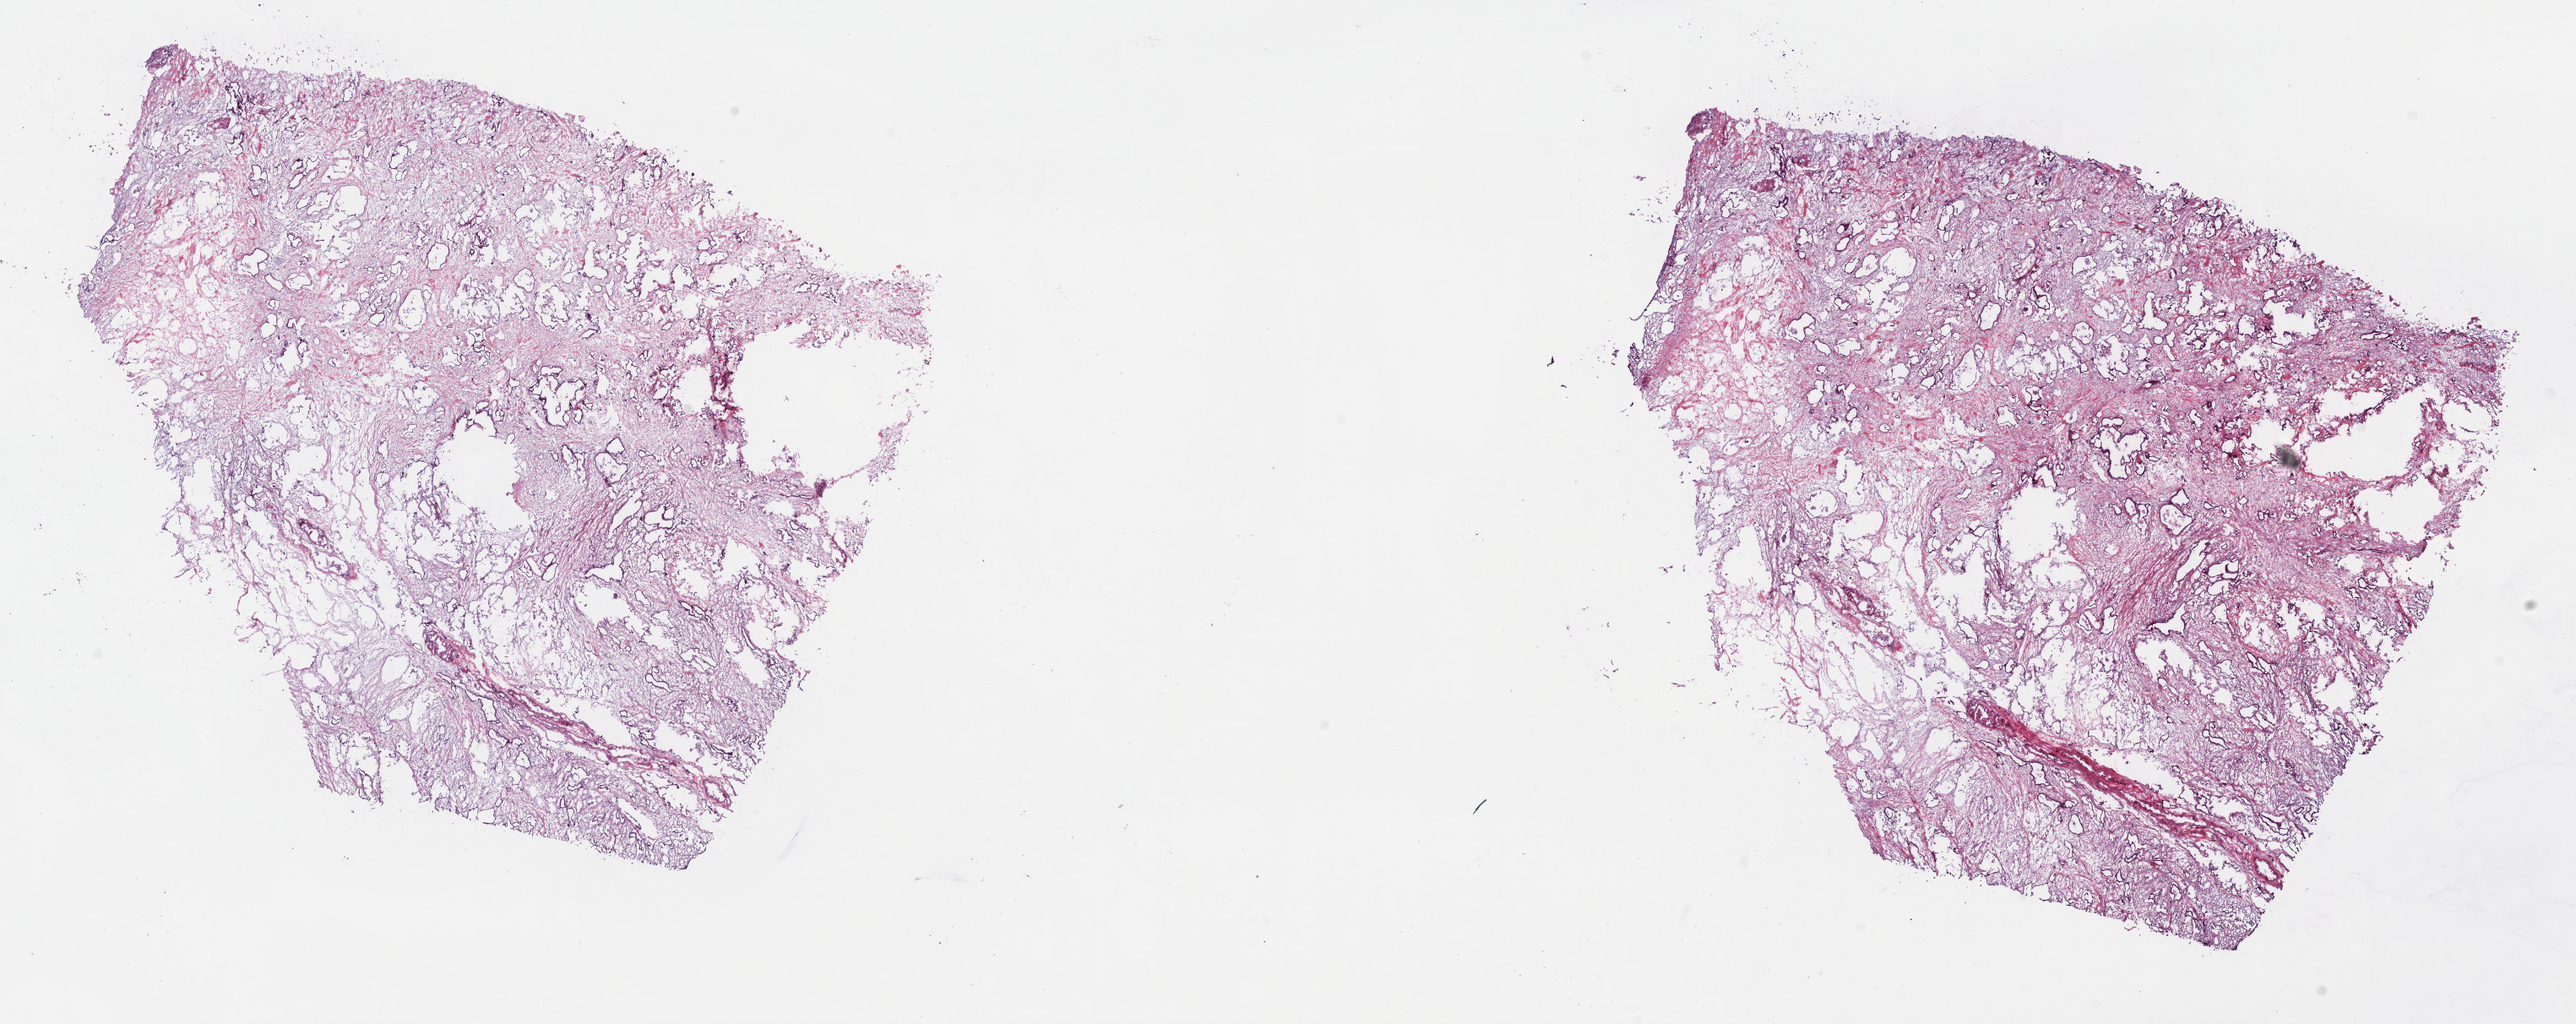
H&E whole-slide image — shown as a low-resolution overview of the whole scanned area (about 24.7 x 9.8 mm), frozen section from the top of the tissue portion, sample: primary tumour, bile duct. Patient: male, age at initial diagnosis 49 years. Histologic grade: G2 (moderately differentiated). Pathologist review of this section (percent, as recorded): tumour cells 65%, tumour nuclei 65%, normal cells 0%, stromal cells 35%, necrosis 0%. Inflammatory infiltration, as recorded: lymphocyte infiltration 3%, monocyte infiltration 1%, neutrophil infiltration 4%.
- TNM: T3 N0 M1
- pathologic diagnosis: Cholangiocarcinoma (extrahepatic bile duct)
- AJCC pathologic stage: IVB (6th edition)